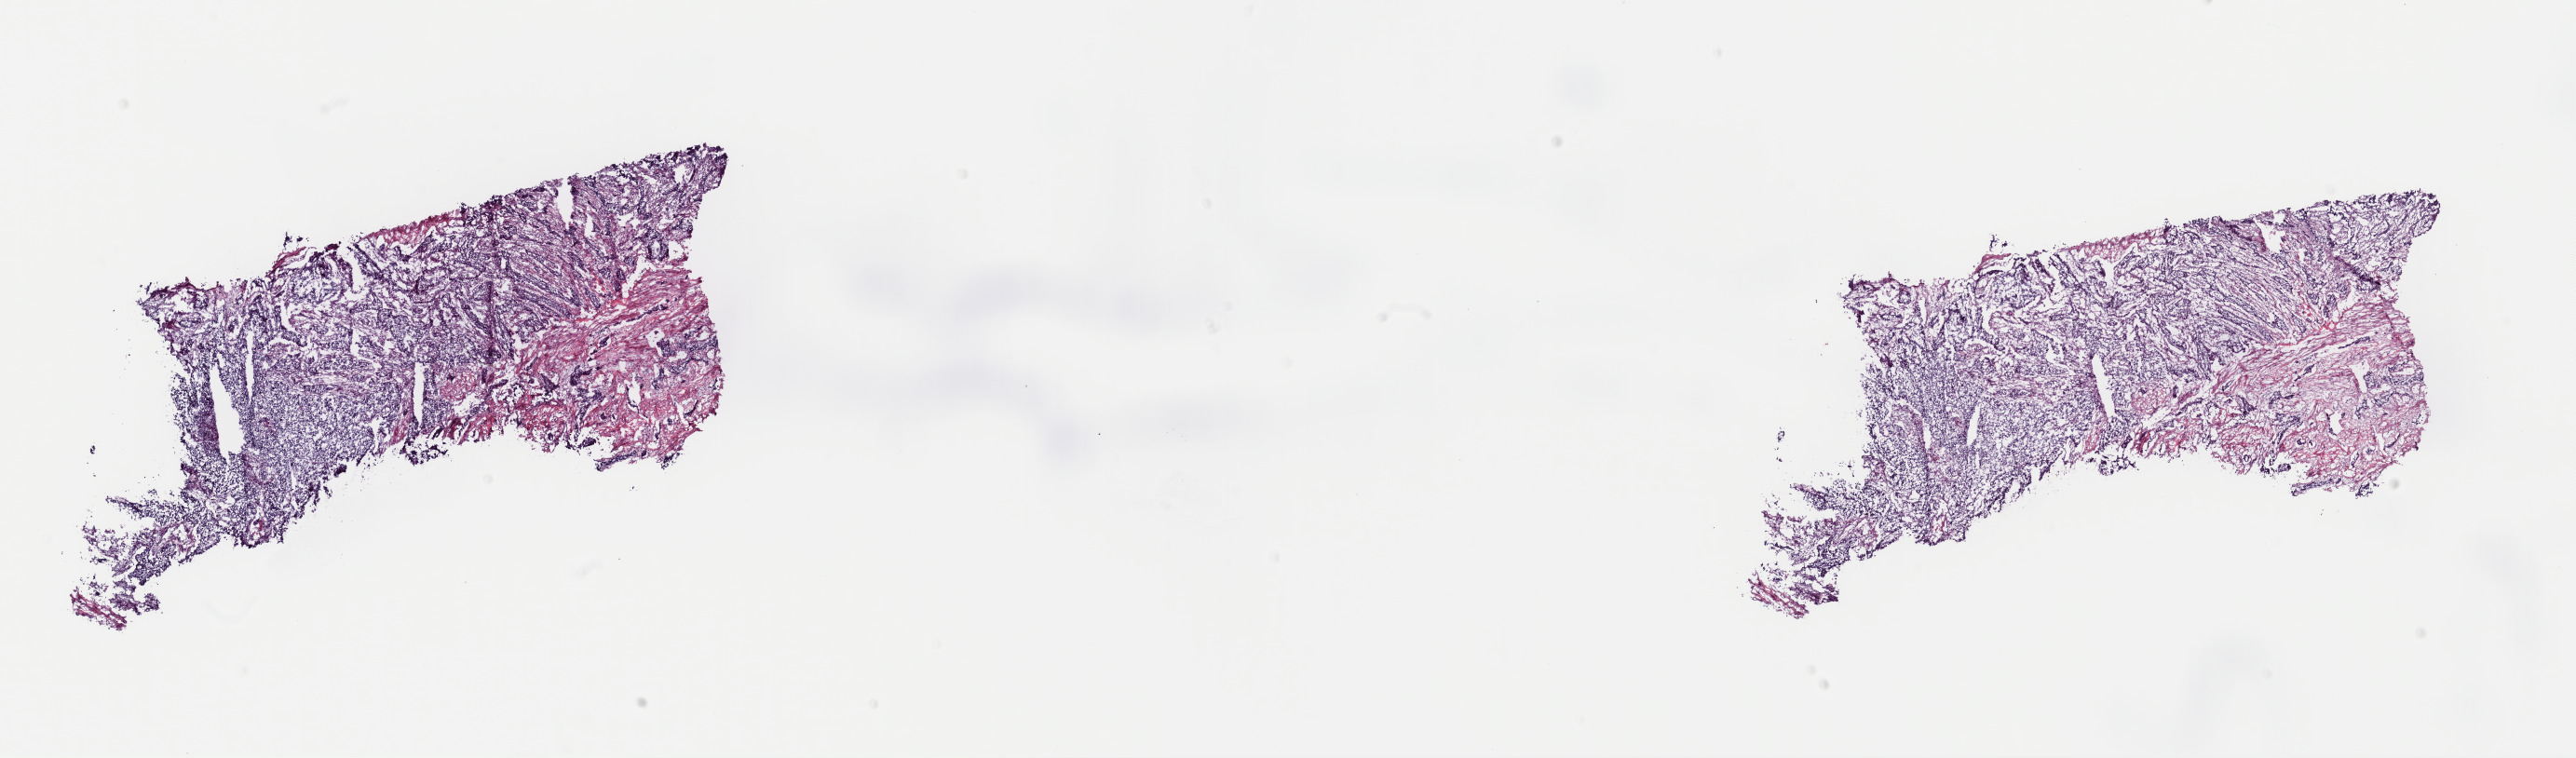
Whole-slide histology image, H&E-stained, shown as a low-resolution overview of the whole scanned area (about 21.9 x 6.4 mm), frozen section from the top of the tissue portion, sample: primary tumour, bladder. Patient: male, age at initial diagnosis 61 years. Histologic grade: high grade. Slide review estimates, as recorded: tumour cells 80%, tumour nuclei 80%, normal cells 0%, stromal cells 20%, necrosis 0%. Inflammatory infiltration, as recorded: lymphocyte infiltration 4%, monocyte infiltration 2%, neutrophil infiltration 2%.
• AJCC pathologic stage: IV
• lymph nodes positive (case pathology): 1 of 2 examined
• histologic diagnosis: Transitional cell carcinoma